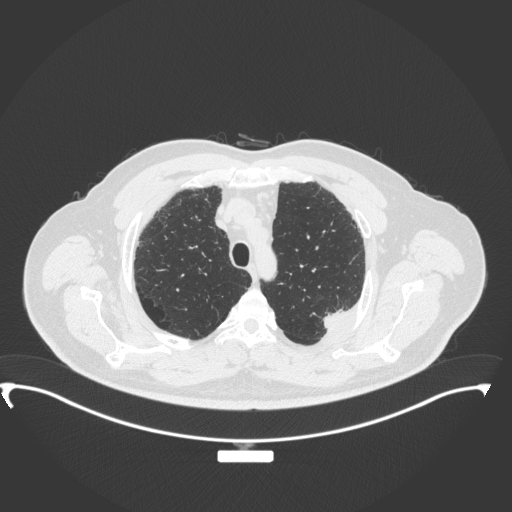
Chest CT, one axial slice; slice 289 of 350 in the series (ordered by position); reconstruction kernel B31f; 120 kVp; lung window (W 1500 / L -600 HU); 512 × 512 image matrix. Patient: male, 64 years. Case-level facts recorded for this patient, not image findings: clinical TNM (as recorded): T1c N1 M1.
Annotated regions visible in this slice (rectangle marked by the reading radiologist):
- lung tumour (recorded histology: adenocarcinoma): bounding box (x1, y1, x2, y2) in pixels: (323, 304, 356, 334)